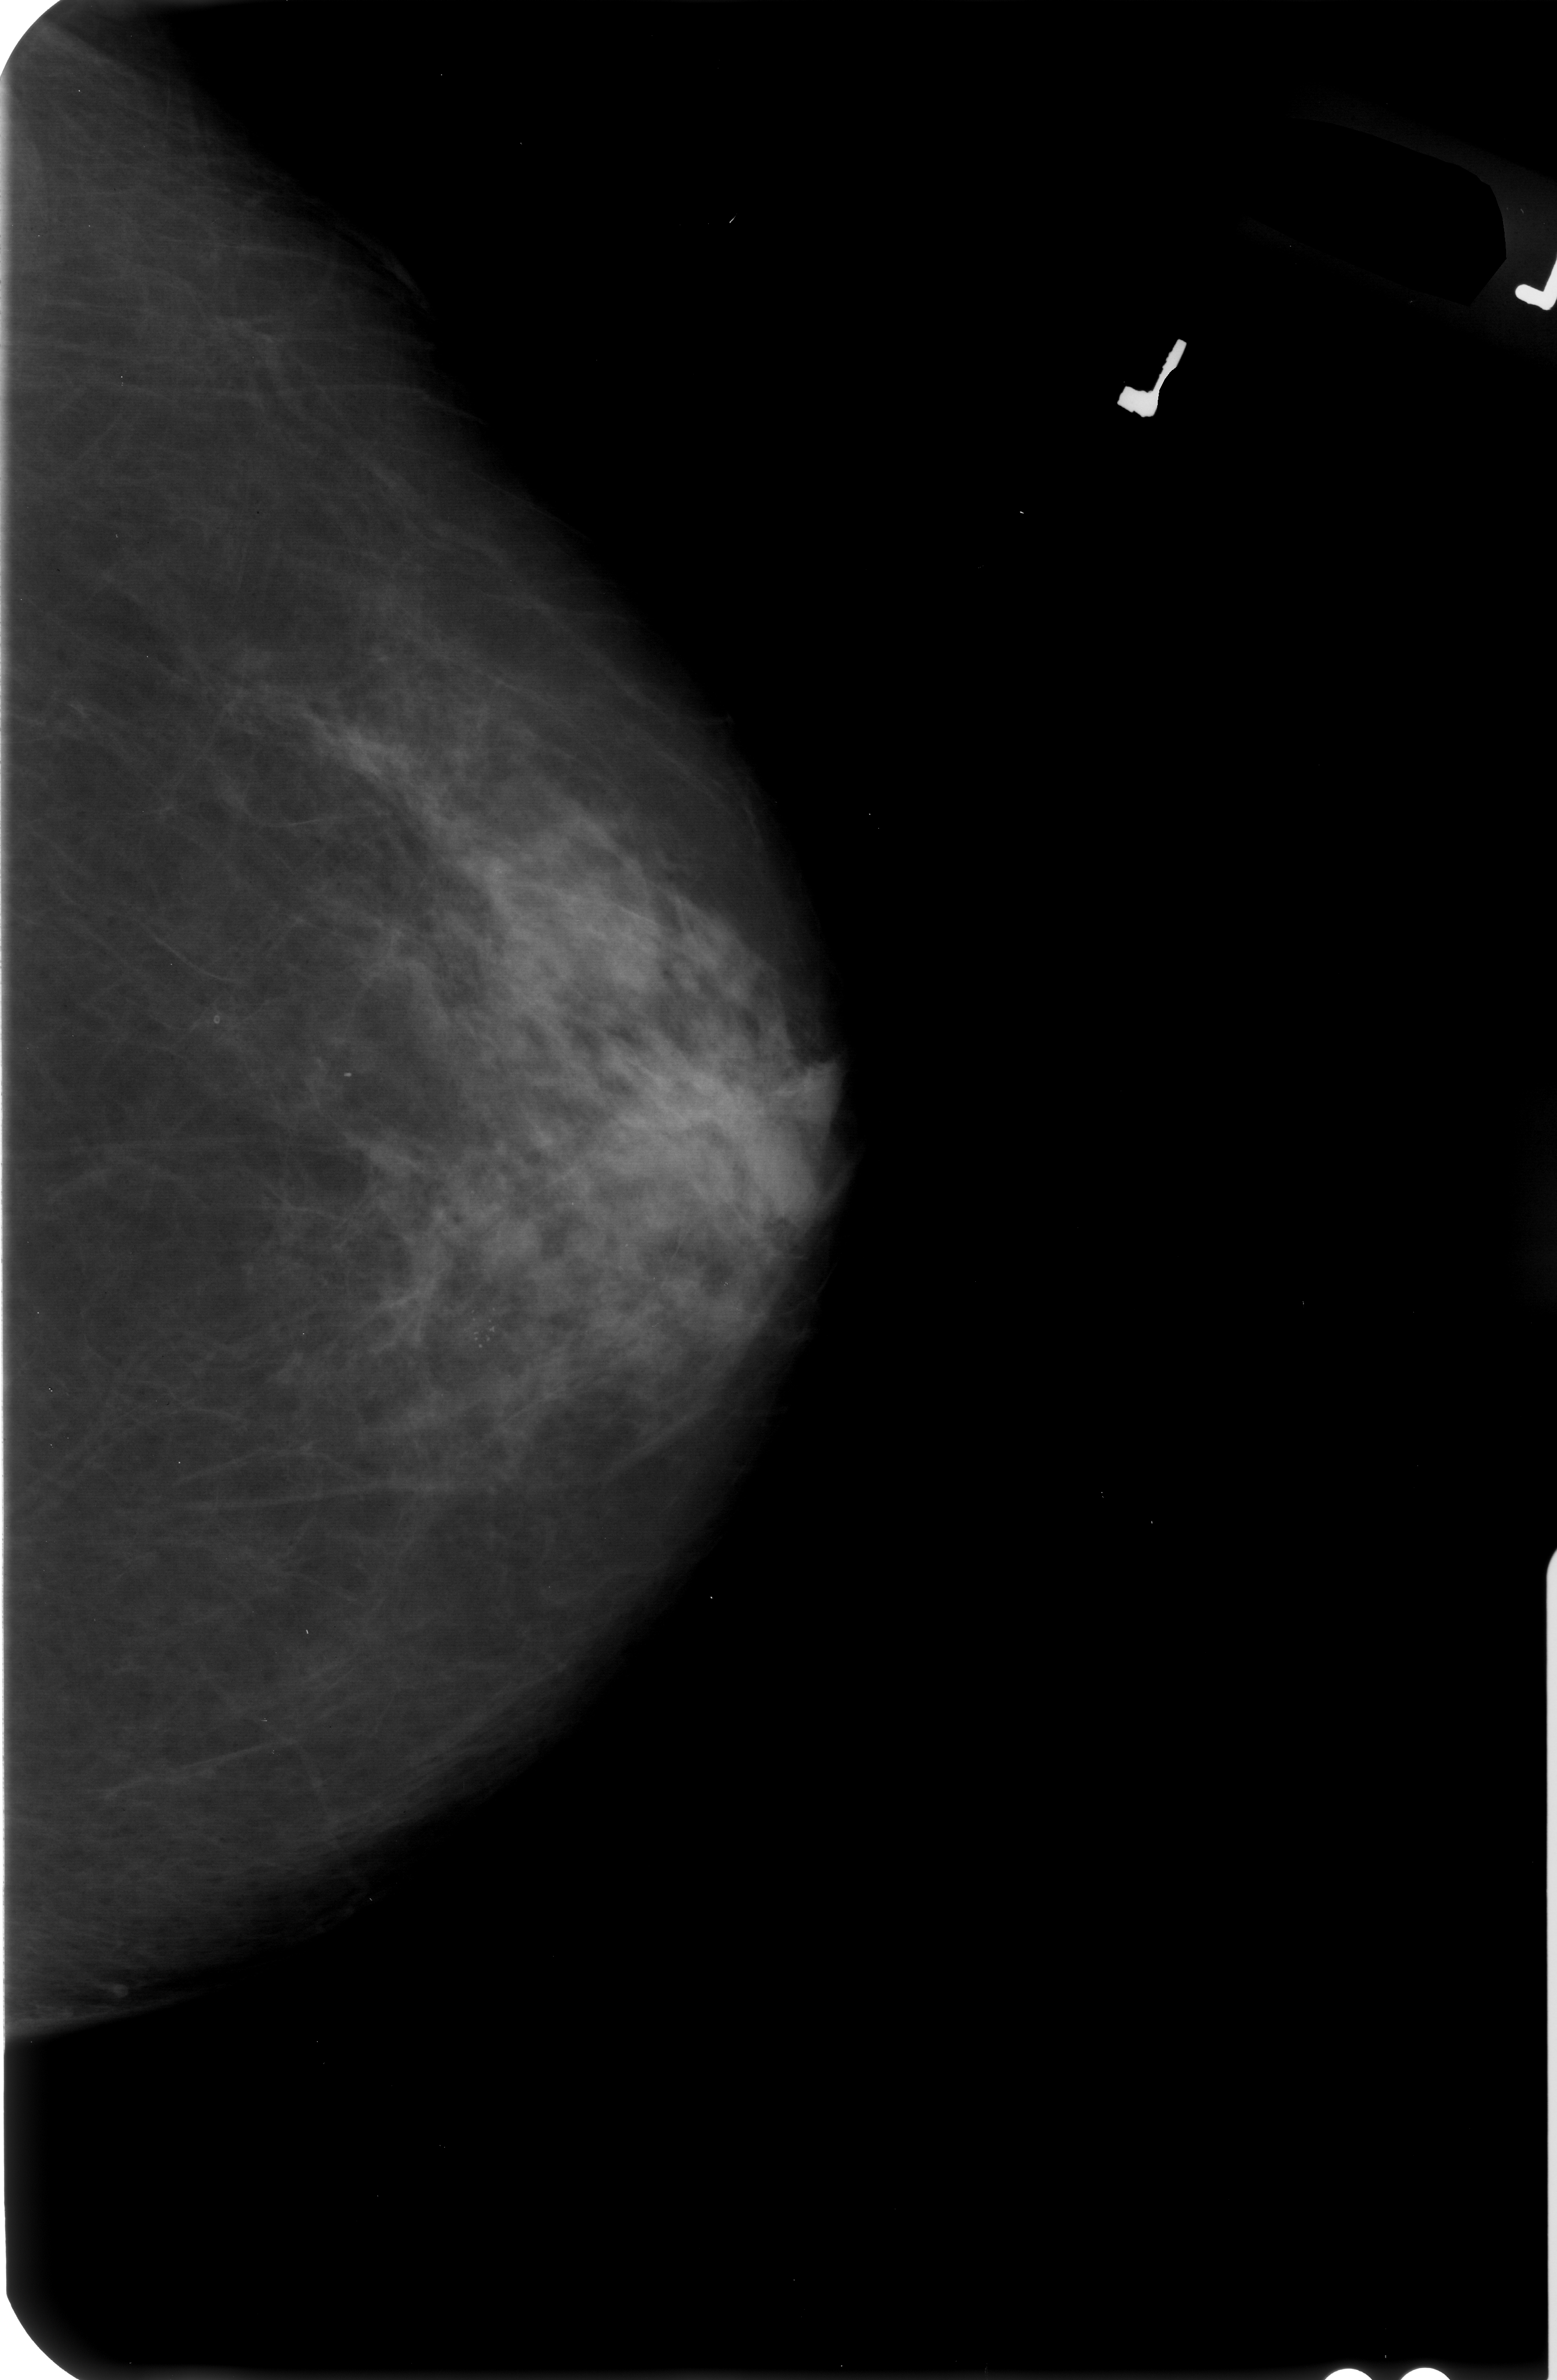
Mammogram (digitized film); left breast; CC view; BI-RADS breast density category 2 (scale 1–4); 1557 × 2380 image matrix.
Expert-marked regions of interest on this film, with their recorded descriptors:
- calcifications, morphology punctate / pleomorphic, distribution clustered; BI-RADS assessment category 4; subtlety rating 3 on a 1 (subtle) to 5 (obvious) scale; pathology (as recorded): malignant: bounding box [x1, y1, x2, y2] px = [435, 1269, 520, 1383]